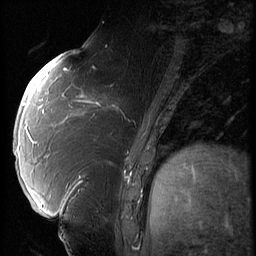
Breast MRI (dynamic contrast-enhanced), one sagittal slice. Position 27 of 66 along the scan axis. 3 images stored at this slice position (order not interpretable as contrast timing). 1.5 T. TE 4.2 ms, TR 9 ms. 2.5 mm slice thickness. 256 × 256 image matrix, field of view 180 × 180 mm. Patient: female, 57 years. Case-level facts recorded for this patient, not image findings: setting: breast cancer imaged before/during neoadjuvant chemotherapy; receptor status: triple-negative.
Annotated regions visible in this slice (semi-automatic segmentation, software-assisted and operator-edited):
- analysis volume of interest (the breast-tissue region the enhancement analysis was run in; not a lesion): box from (x=86, y=74) to (x=138, y=129) px
- tumour enhancement mask (voxels above the 140 % enhancement threshold inside the analysis volume of interest): (x=92, y=95)–(x=118, y=110)